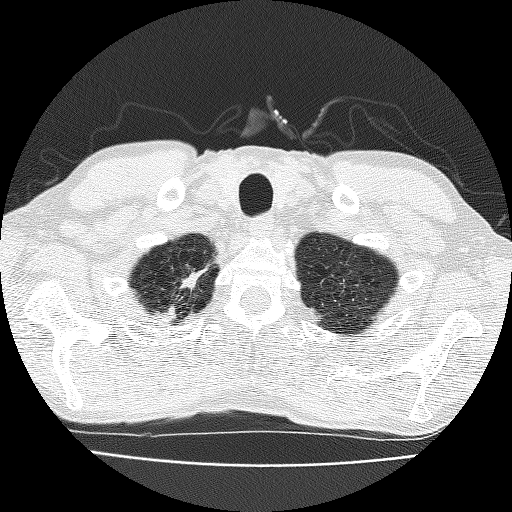
Chest CT (low-dose screening protocol), one axial image; third annual screen; lung window (W 1500 / L -600 HU); 2 mm slice thickness; lung (sharp) reconstruction kernel (FC51); slice 24 of 185 in the series; 512 × 512 image matrix. Male, age 63 years at enrolment. Current smoker at enrolment.
Expert-annotated lung lesion, bounding box <147,258,227,325> (left, top, right, bottom; pixels). Reader record for this screening exam (exam-level; its link to the box is not recorded): non-calcified nodule or mass ≥4 mm, right upper lobe, 17 × 10 mm, spiculated (stellate) margins, soft tissue attenuation, pre-existing on the prior screen: yes; interval growth: yes. Official screen result: positive, other. Participant outcome: lung cancer diagnosed 28 days after this screen — adenocarcinoma, NOS, right upper lobe, moderately differentiated (G2), stage IIIB (AJCC 6th edition), 17 mm at pathology.